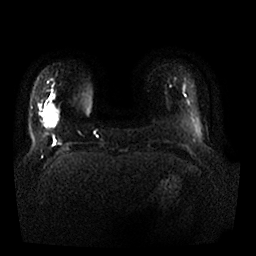
Breast MRI, one axial slice; position 4 of 25 along the scan axis; diffusion-weighted series; image 2 of 4 stored at this slice position (different b-values; order by instance number); 1.5 T; 4 mm slice thickness; 256 × 256 image matrix, field of view 350 × 350 mm. Female patient.
Annotated regions visible in this slice (outlined manually by an expert reader):
- tumour on diffusion-weighted imaging: bounding box <46,104,58,127> (left, top, right, bottom; pixels)